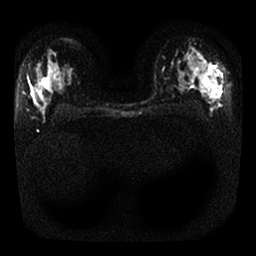
Breast MRI, one axial slice. Position 18 of 25 along the scan axis. Diffusion-weighted series; image 2 of 4 stored at this slice position (different b-values; order by instance number). 1.5 T. 256 × 256 image matrix, field of view 320 × 320 mm. Female patient.
Structures marked on this image (expert manual segmentation):
- tumour on diffusion-weighted imaging: bounding box (x1, y1, x2, y2) in pixels: (196, 60, 214, 77)